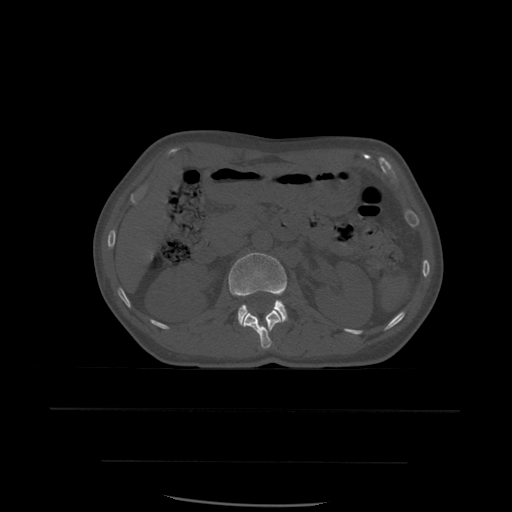
CT including the spine, one axial slice; position 236 of 574 along the scan axis; bone window (W 1800 / L 400 HU); 1.25 mm slice thickness; 512 × 512 image matrix, field of view 392 × 392 mm. Patient age 48 years. From the clinical record (not read from this slice): primary cancer: lung; vertebrae with lytic lesions (as recorded): T11.
Outlined on this slice (semi-automatically segmented with operator editing):
- L1 vertebra: bounding box [x1, y1, x2, y2] px = [242, 310, 284, 350]
- L2 vertebra: [229, 253, 288, 326]